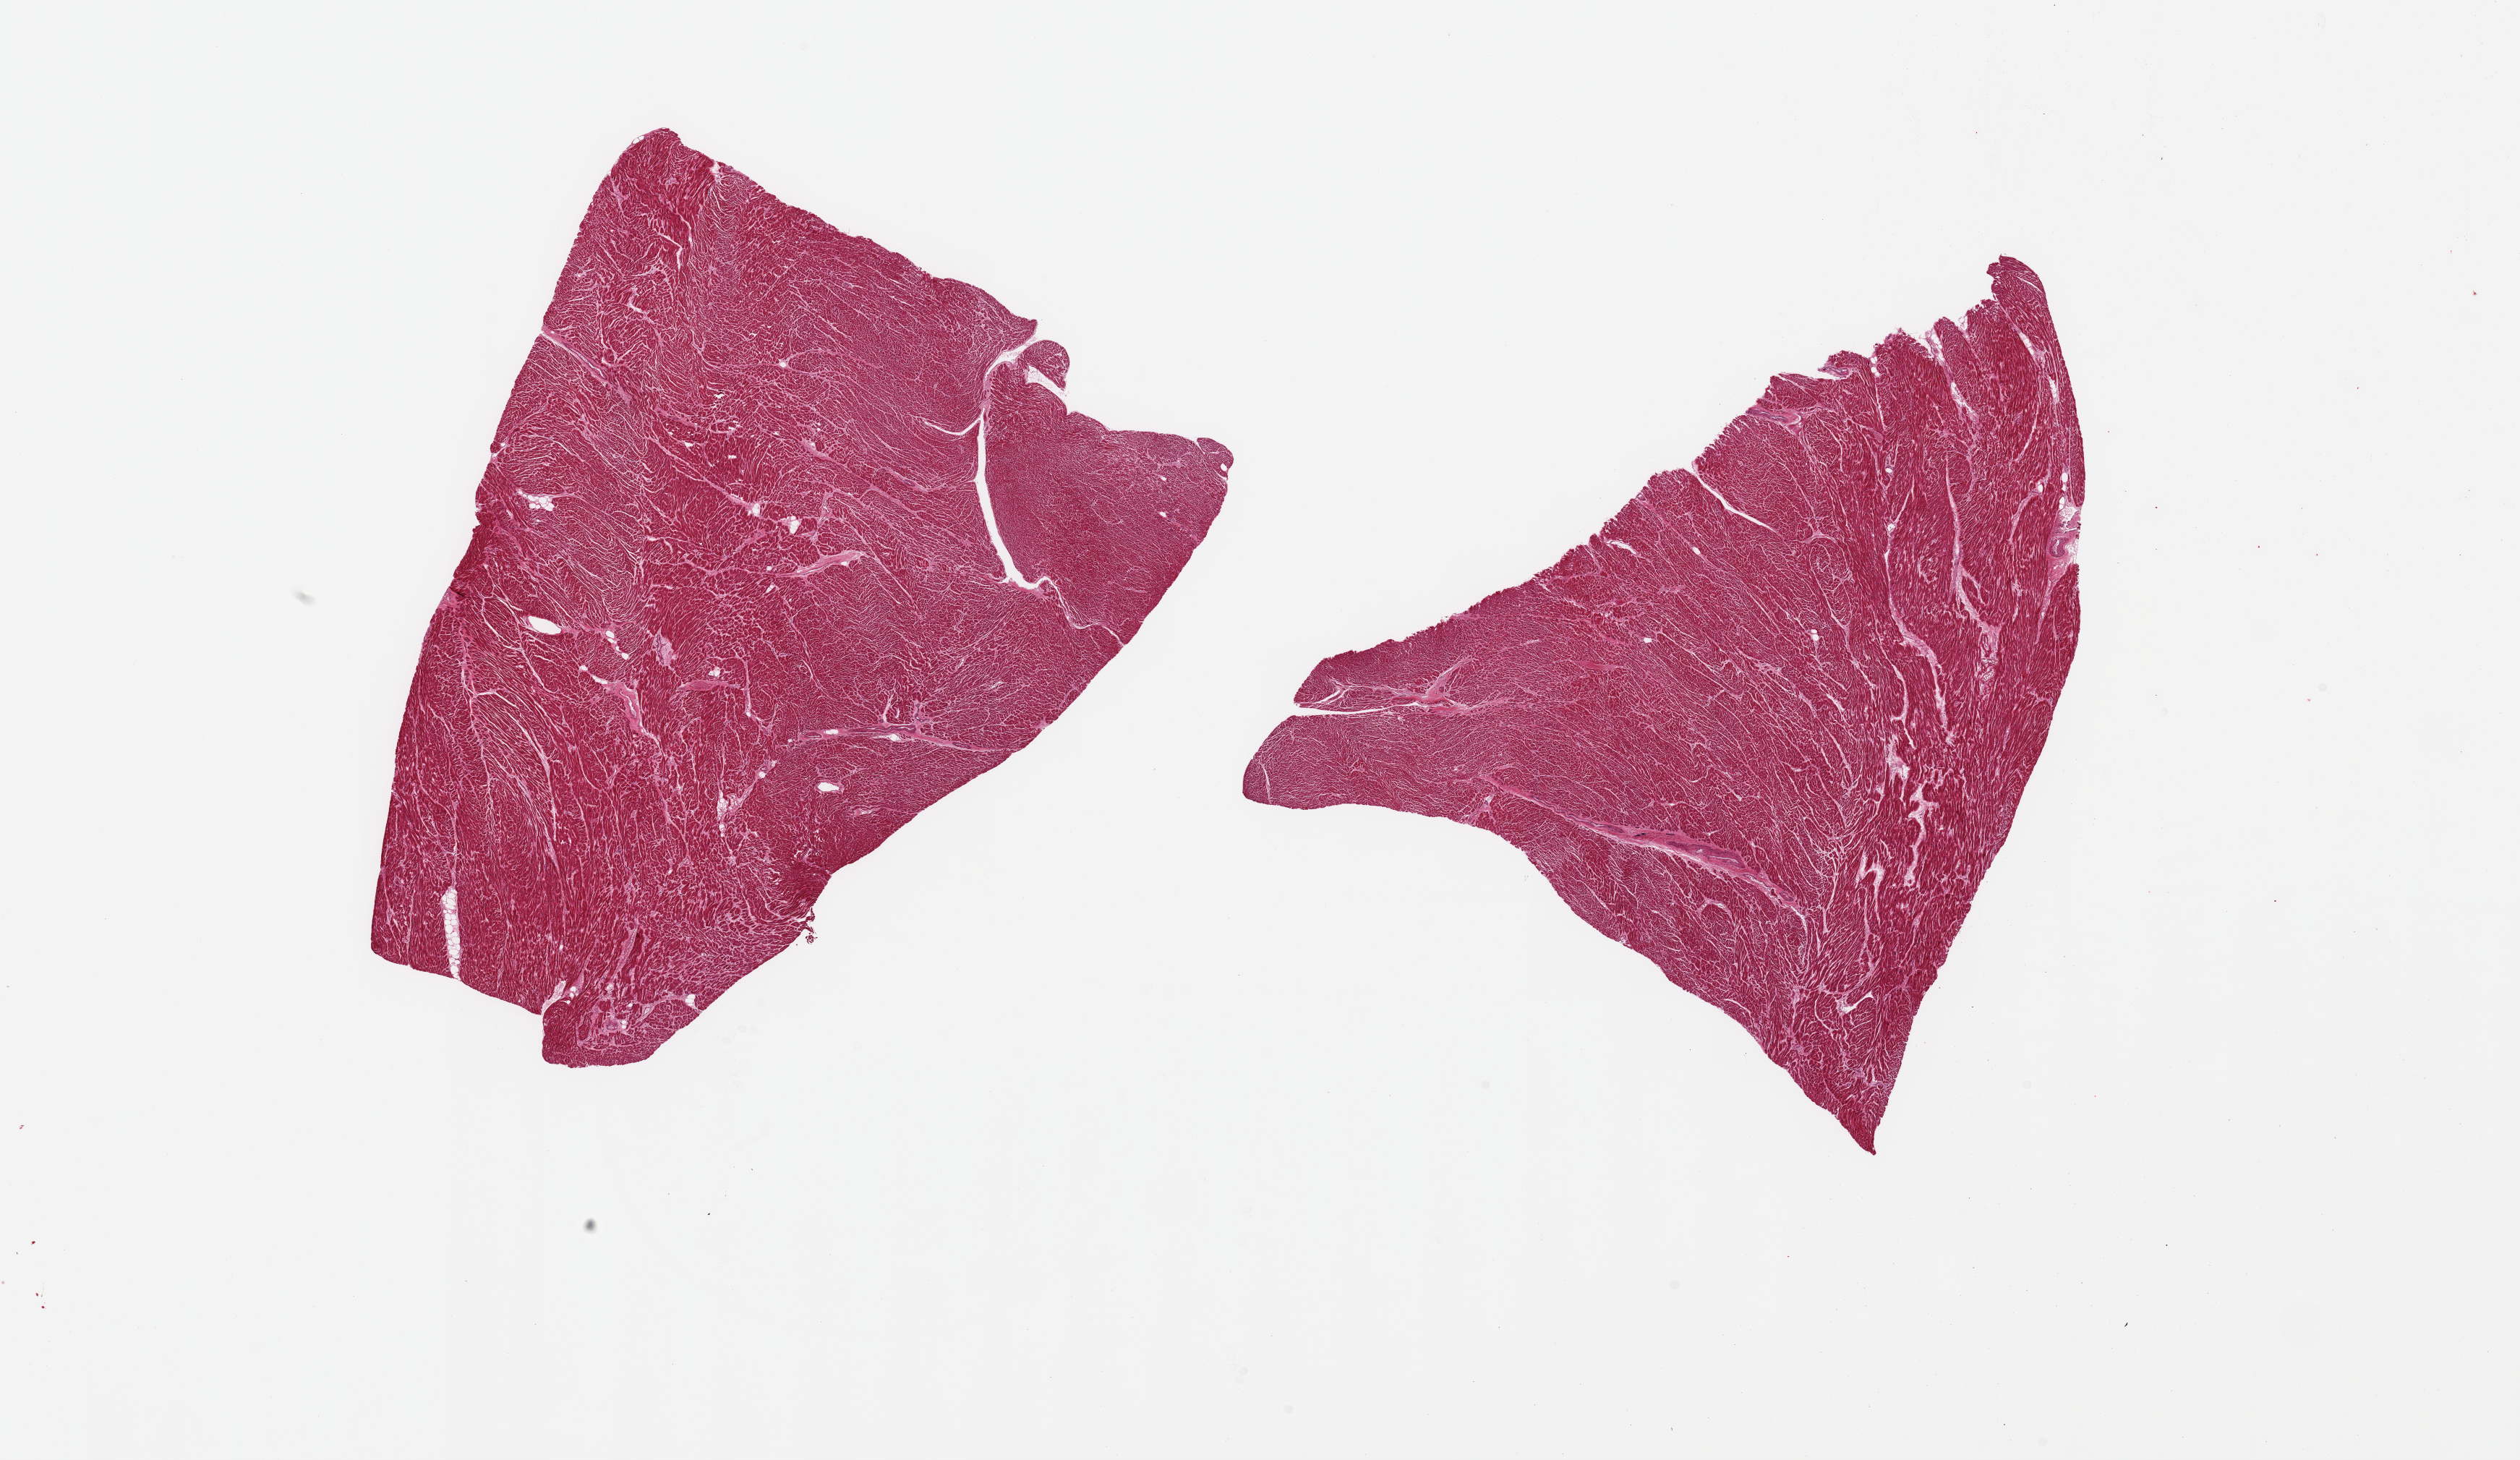
Digitized hematoxylin and eosin (H&E)-stained section, whole scanned area (about 27.6 x 16.0 mm) shown as a low-resolution overview, PAXgene-fixed paraffin-embedded (PFPE) section, target tissue: heart, donor tissue sample. Male donor.
Reviewer comment on this tissue sample: 2 pieces, mild interstitial fibrosis.